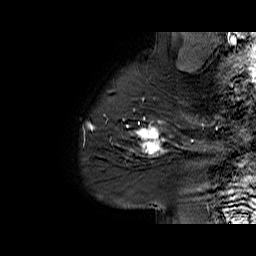
Breast MRI (dynamic contrast-enhanced), one sagittal slice. Slice 53 of 60 in the series (ordered by position). Dynamic contrast-enhanced series, time point 2 of 6 at this slice position (early post-contrast). 1.5 T. TE 6.1 ms, TR 32.9 ms. 4 mm slice thickness. 256 × 256 image matrix. Female patient. From the clinical record (not read from this slice): setting: breast cancer imaged before/during neoadjuvant chemotherapy; receptor status: HER2-positive.
Structures marked on this image (semi-automatic segmentation, software-assisted and operator-edited):
- analysis volume of interest (the breast-tissue region the enhancement analysis was run in; not a lesion): bounding box <127,95,194,165> (left, top, right, bottom; pixels)
- tumour enhancement mask (voxels above the 100 % enhancement threshold inside the analysis volume of interest): <127,98,193,154>